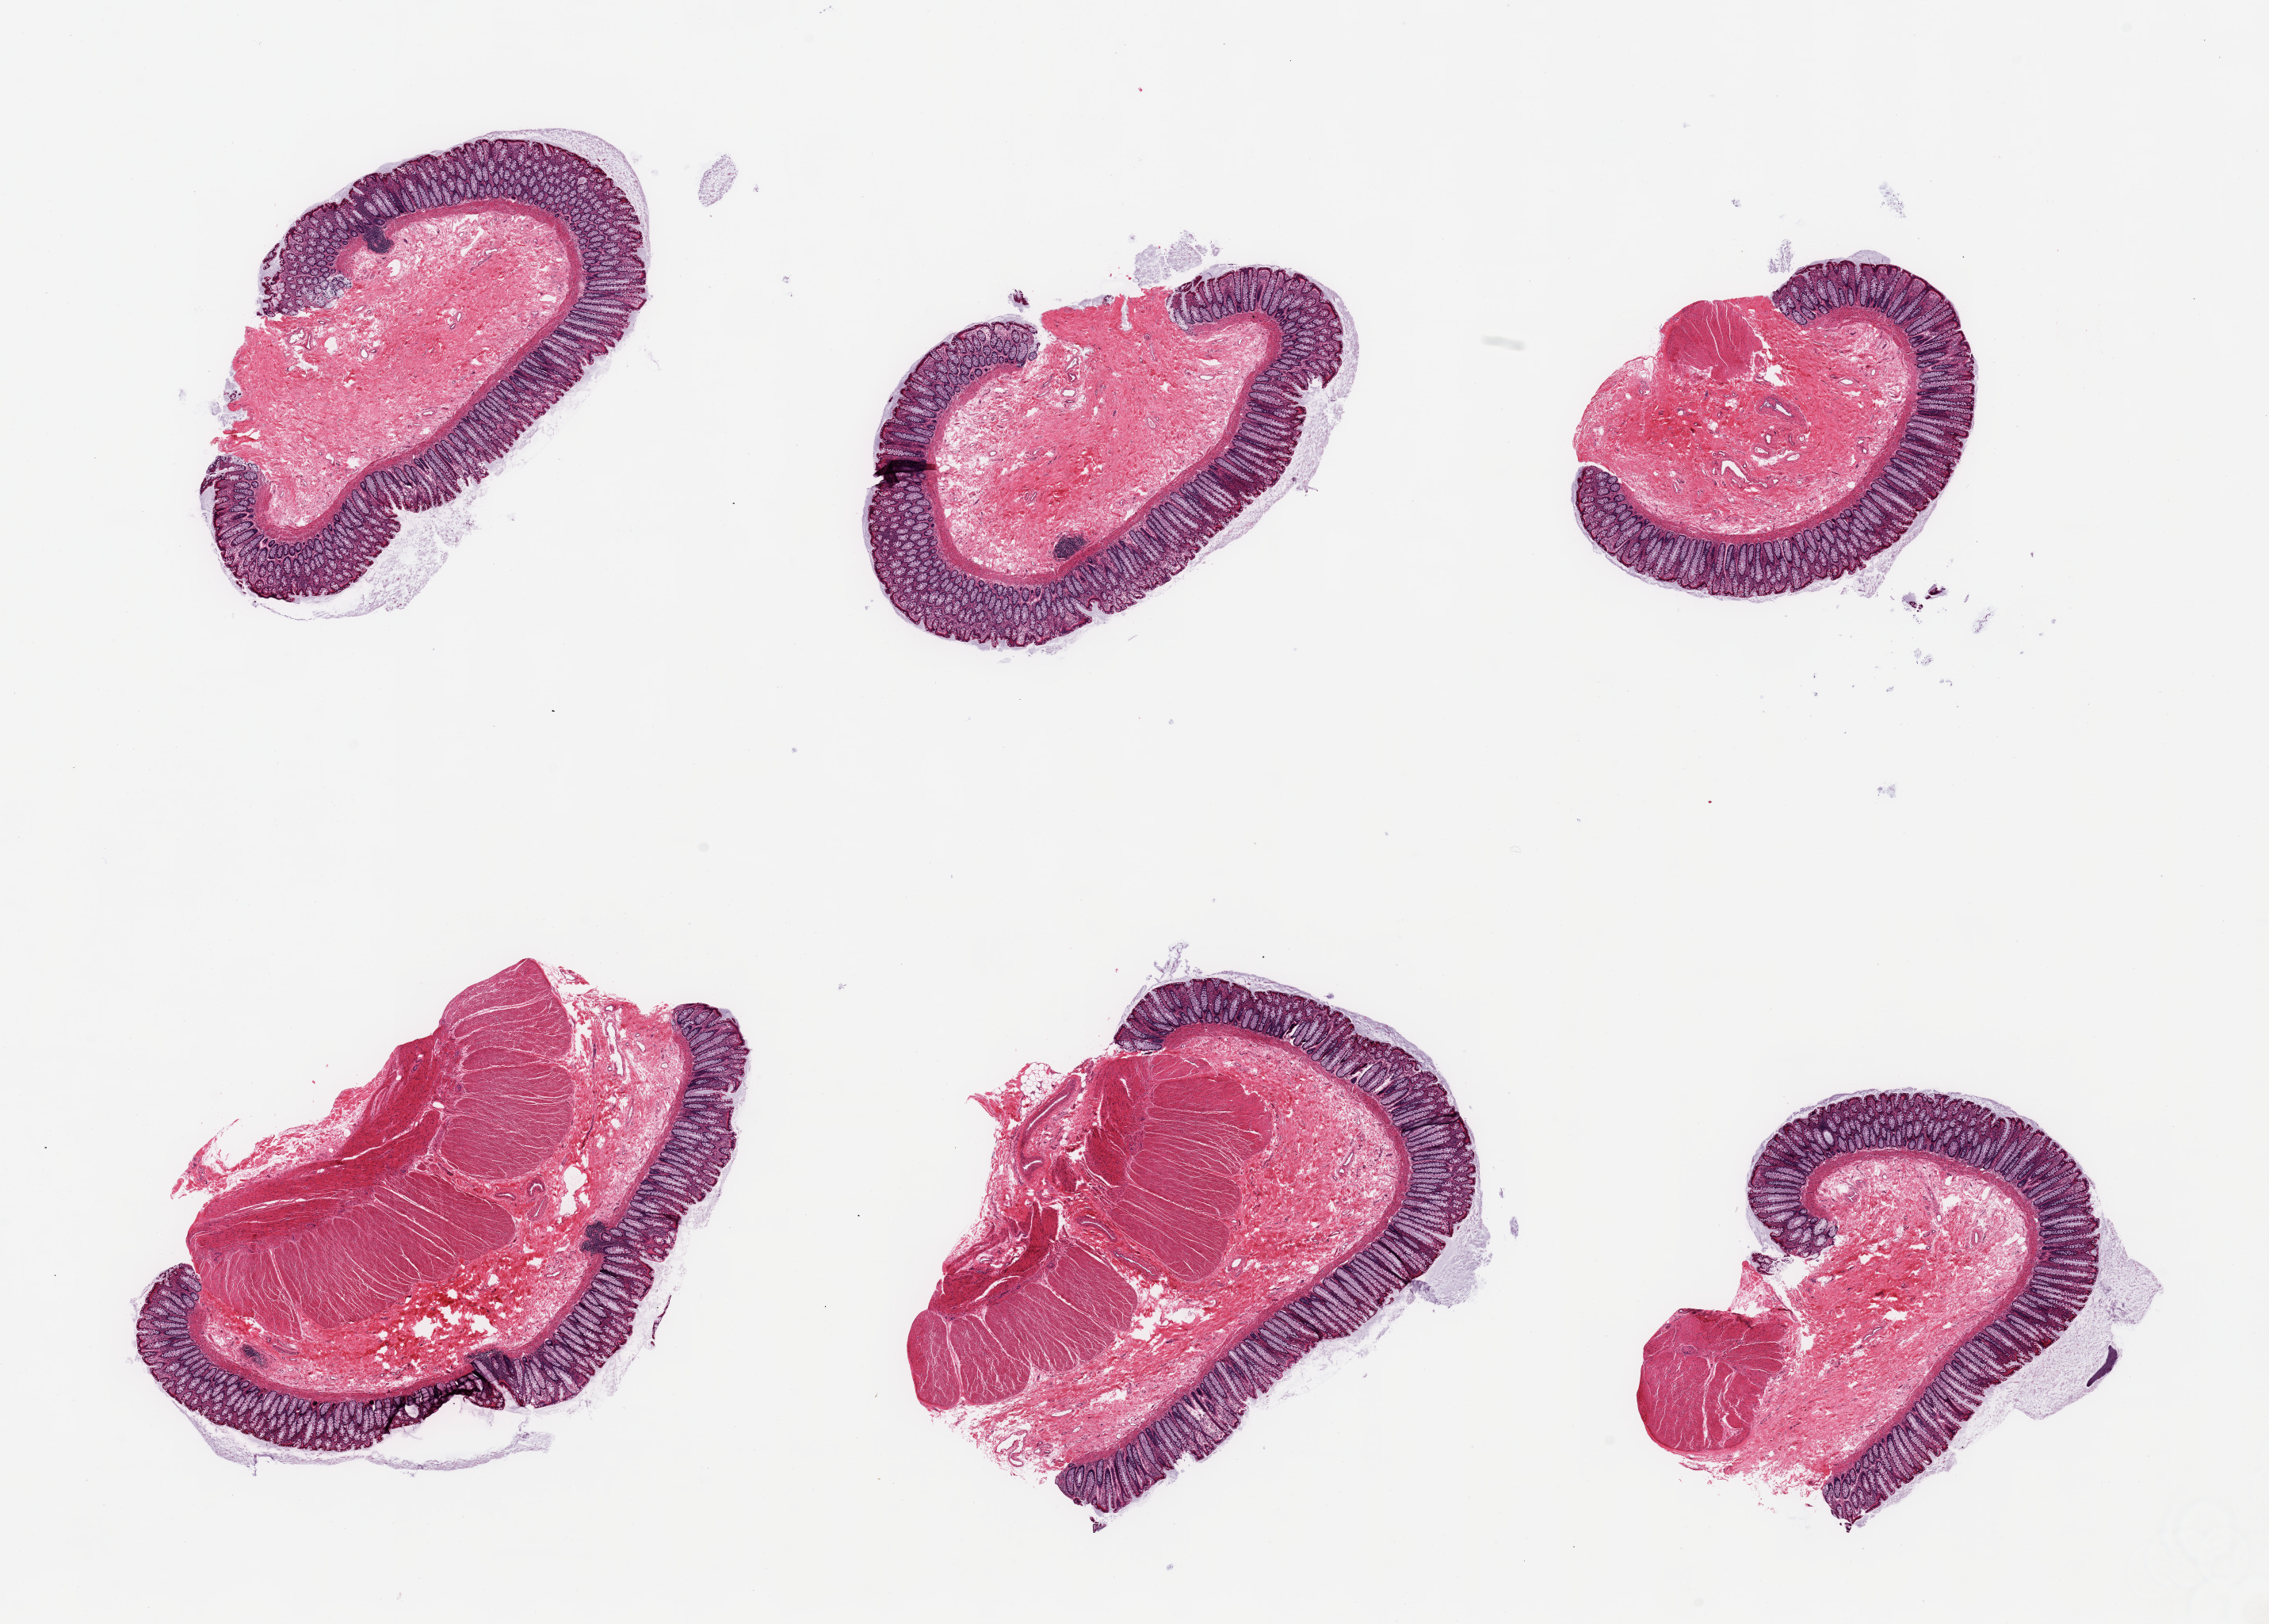
Digitized hematoxylin and eosin (H&E)-stained section, brightfield, low-resolution overview of the scanned area, about 22.6 x 16.2 mm. PAXgene-fixed paraffin-embedded (PFPE) section. Section of ileum (target tissue). Tissue donor sample. Donor sex: female.
Pathologist's review note for this sample: 6 pieces, sections of colon, not ileum.